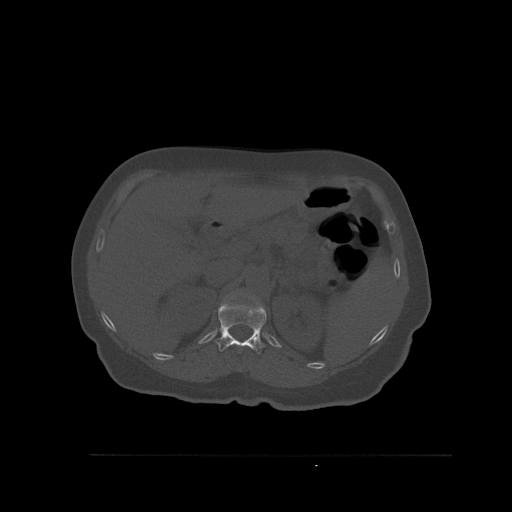
CT including the spine, one axial slice; slice 284 of 527 in the series (ordered by position); bone window (W 1800 / L 400 HU); 1.5 mm slice thickness; 512 × 512 image matrix, field of view 470 × 470 mm. Patient: female, 73 years. From the clinical record (not read from this slice): primary cancer: breast; vertebrae with lytic lesions (as recorded): L2.
Annotated regions visible in this slice (semi-automatic segmentation, software-assisted and operator-edited):
- T12 vertebra: bounding box [x1, y1, x2, y2] px = [215, 301, 267, 354]